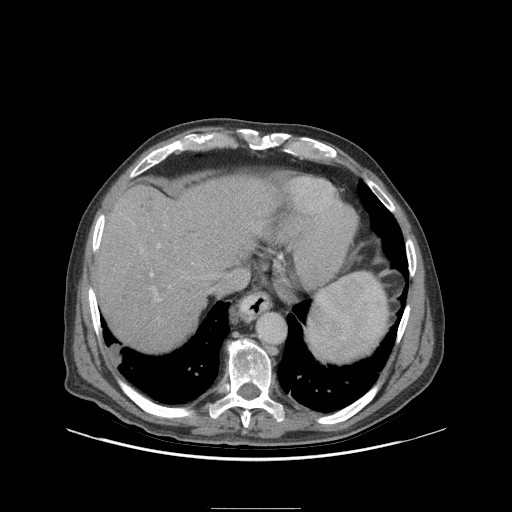
Contrast-enhanced abdominal CT (liver protocol), one axial slice. Position 83 of 105 along the scan axis. Reconstruction kernel STANDARD. 140 kVp. Soft-tissue window (W 400 / L 40 HU). 2.5 mm slice thickness. 512 × 512 image matrix, field of view 440 × 440 mm. From the clinical record (not read from this slice): diagnosis: hepatocellular carcinoma (patient treated with transarterial chemoembolisation; whether this scan precedes or follows treatment is not stated here); TNM stage (as recorded): Stage-I; Child-Pugh class: A; tumour size: 5.1 cm.
Outlined on this slice (semi-automatically segmented with operator editing):
- abdominal aorta: box from (x=258, y=314) to (x=285, y=343) px
- liver parenchyma outside the tumour (the mass and vessels are separate outlines, so this box may not span the whole liver): (x=94, y=176)–(x=278, y=350)
- liver vessels: (x=150, y=244)–(x=161, y=300)